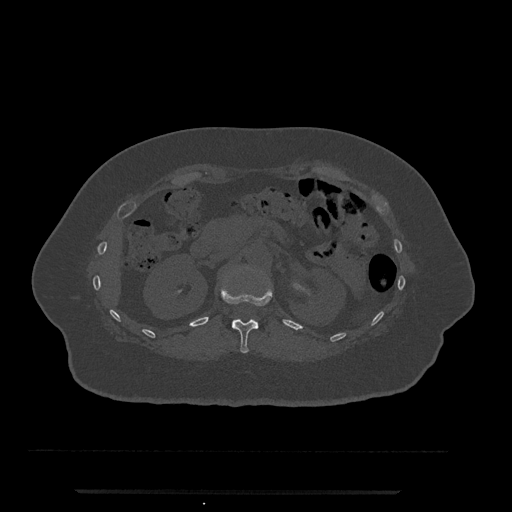
CT including the spine, one axial slice. Position 150 of 797 along the scan axis. Bone window (W 1800 / L 400 HU). 512 × 512 image matrix, field of view 440 × 440 mm. Female patient, age 51 years. Case-level facts recorded for this patient, not image findings: primary cancer: neuro.
Structures marked on this image (semi-automatically segmented with operator editing):
- T12 vertebra: bounding box <220,285,273,353> (left, top, right, bottom; pixels)